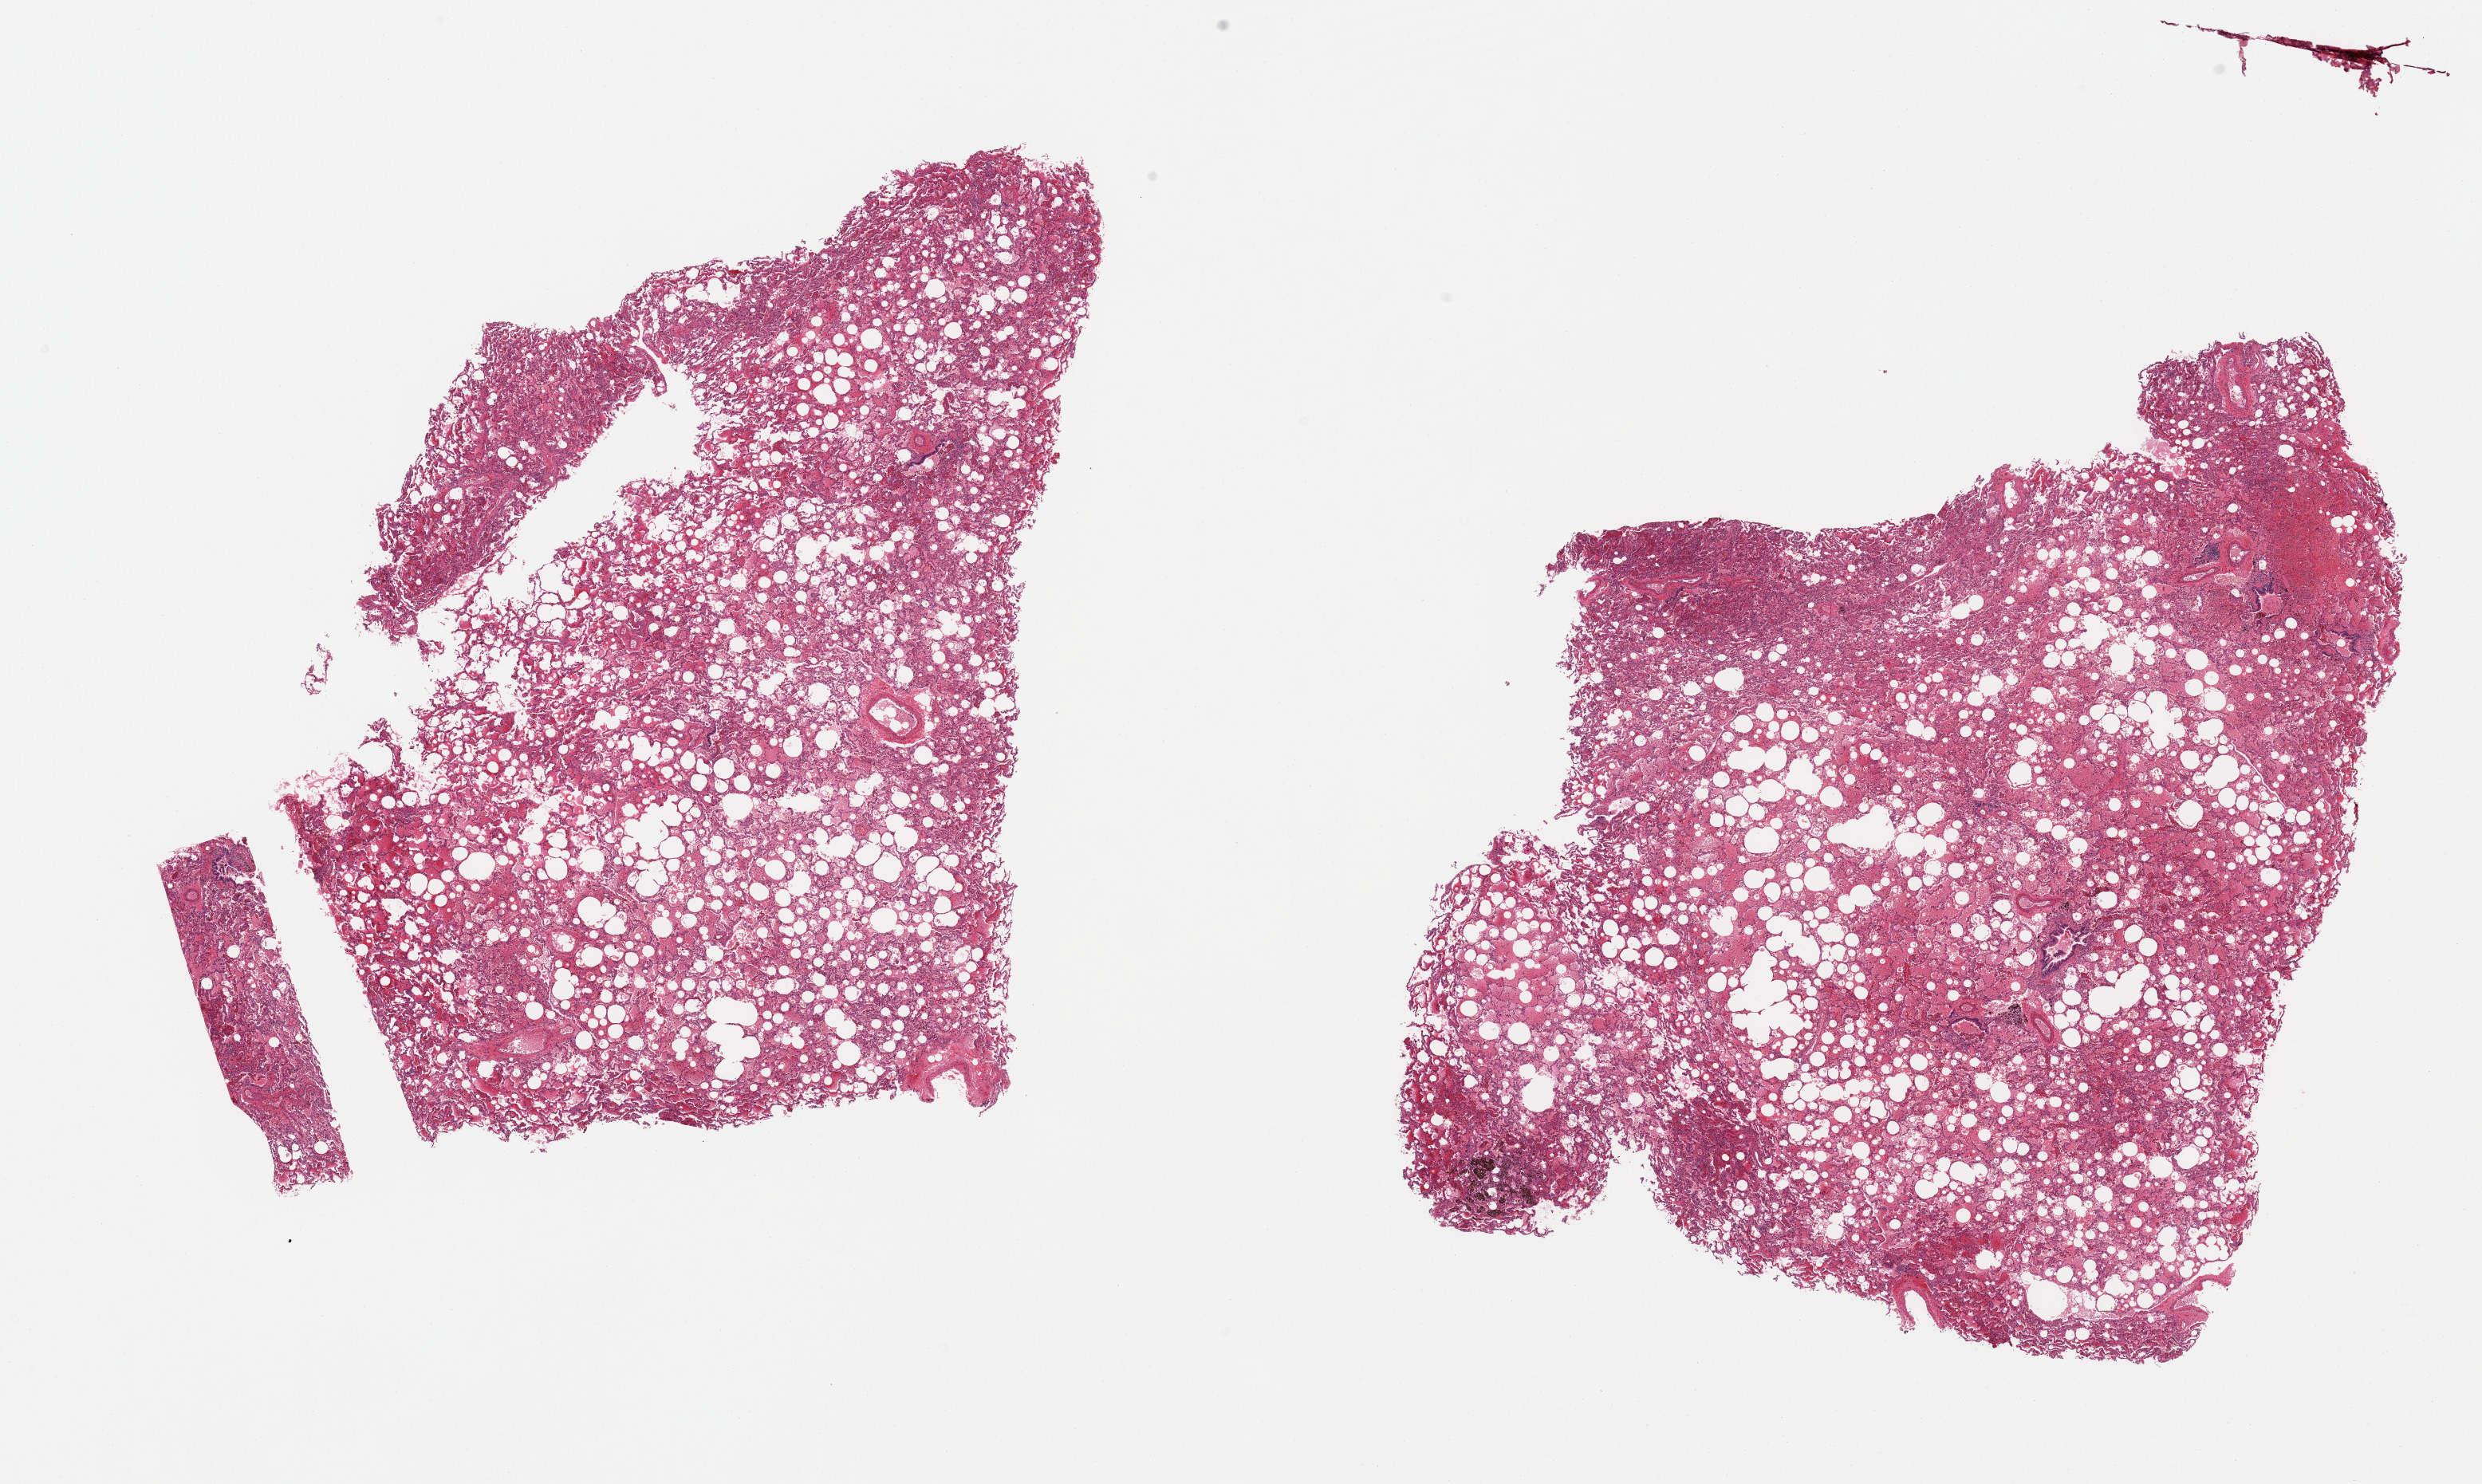
H&E whole-slide image — a low-resolution overview of the entire scanned area, about 24.6 x 14.7 mm (slide scanned at 20x). PAXgene-fixed, paraffin-embedded tissue. Section of lung (target tissue). Donor tissue sample.
Reviewer comment on this tissue sample: 2 pieces, moderate congestiona; pathcy acute pneumonia, focally necrotizing.